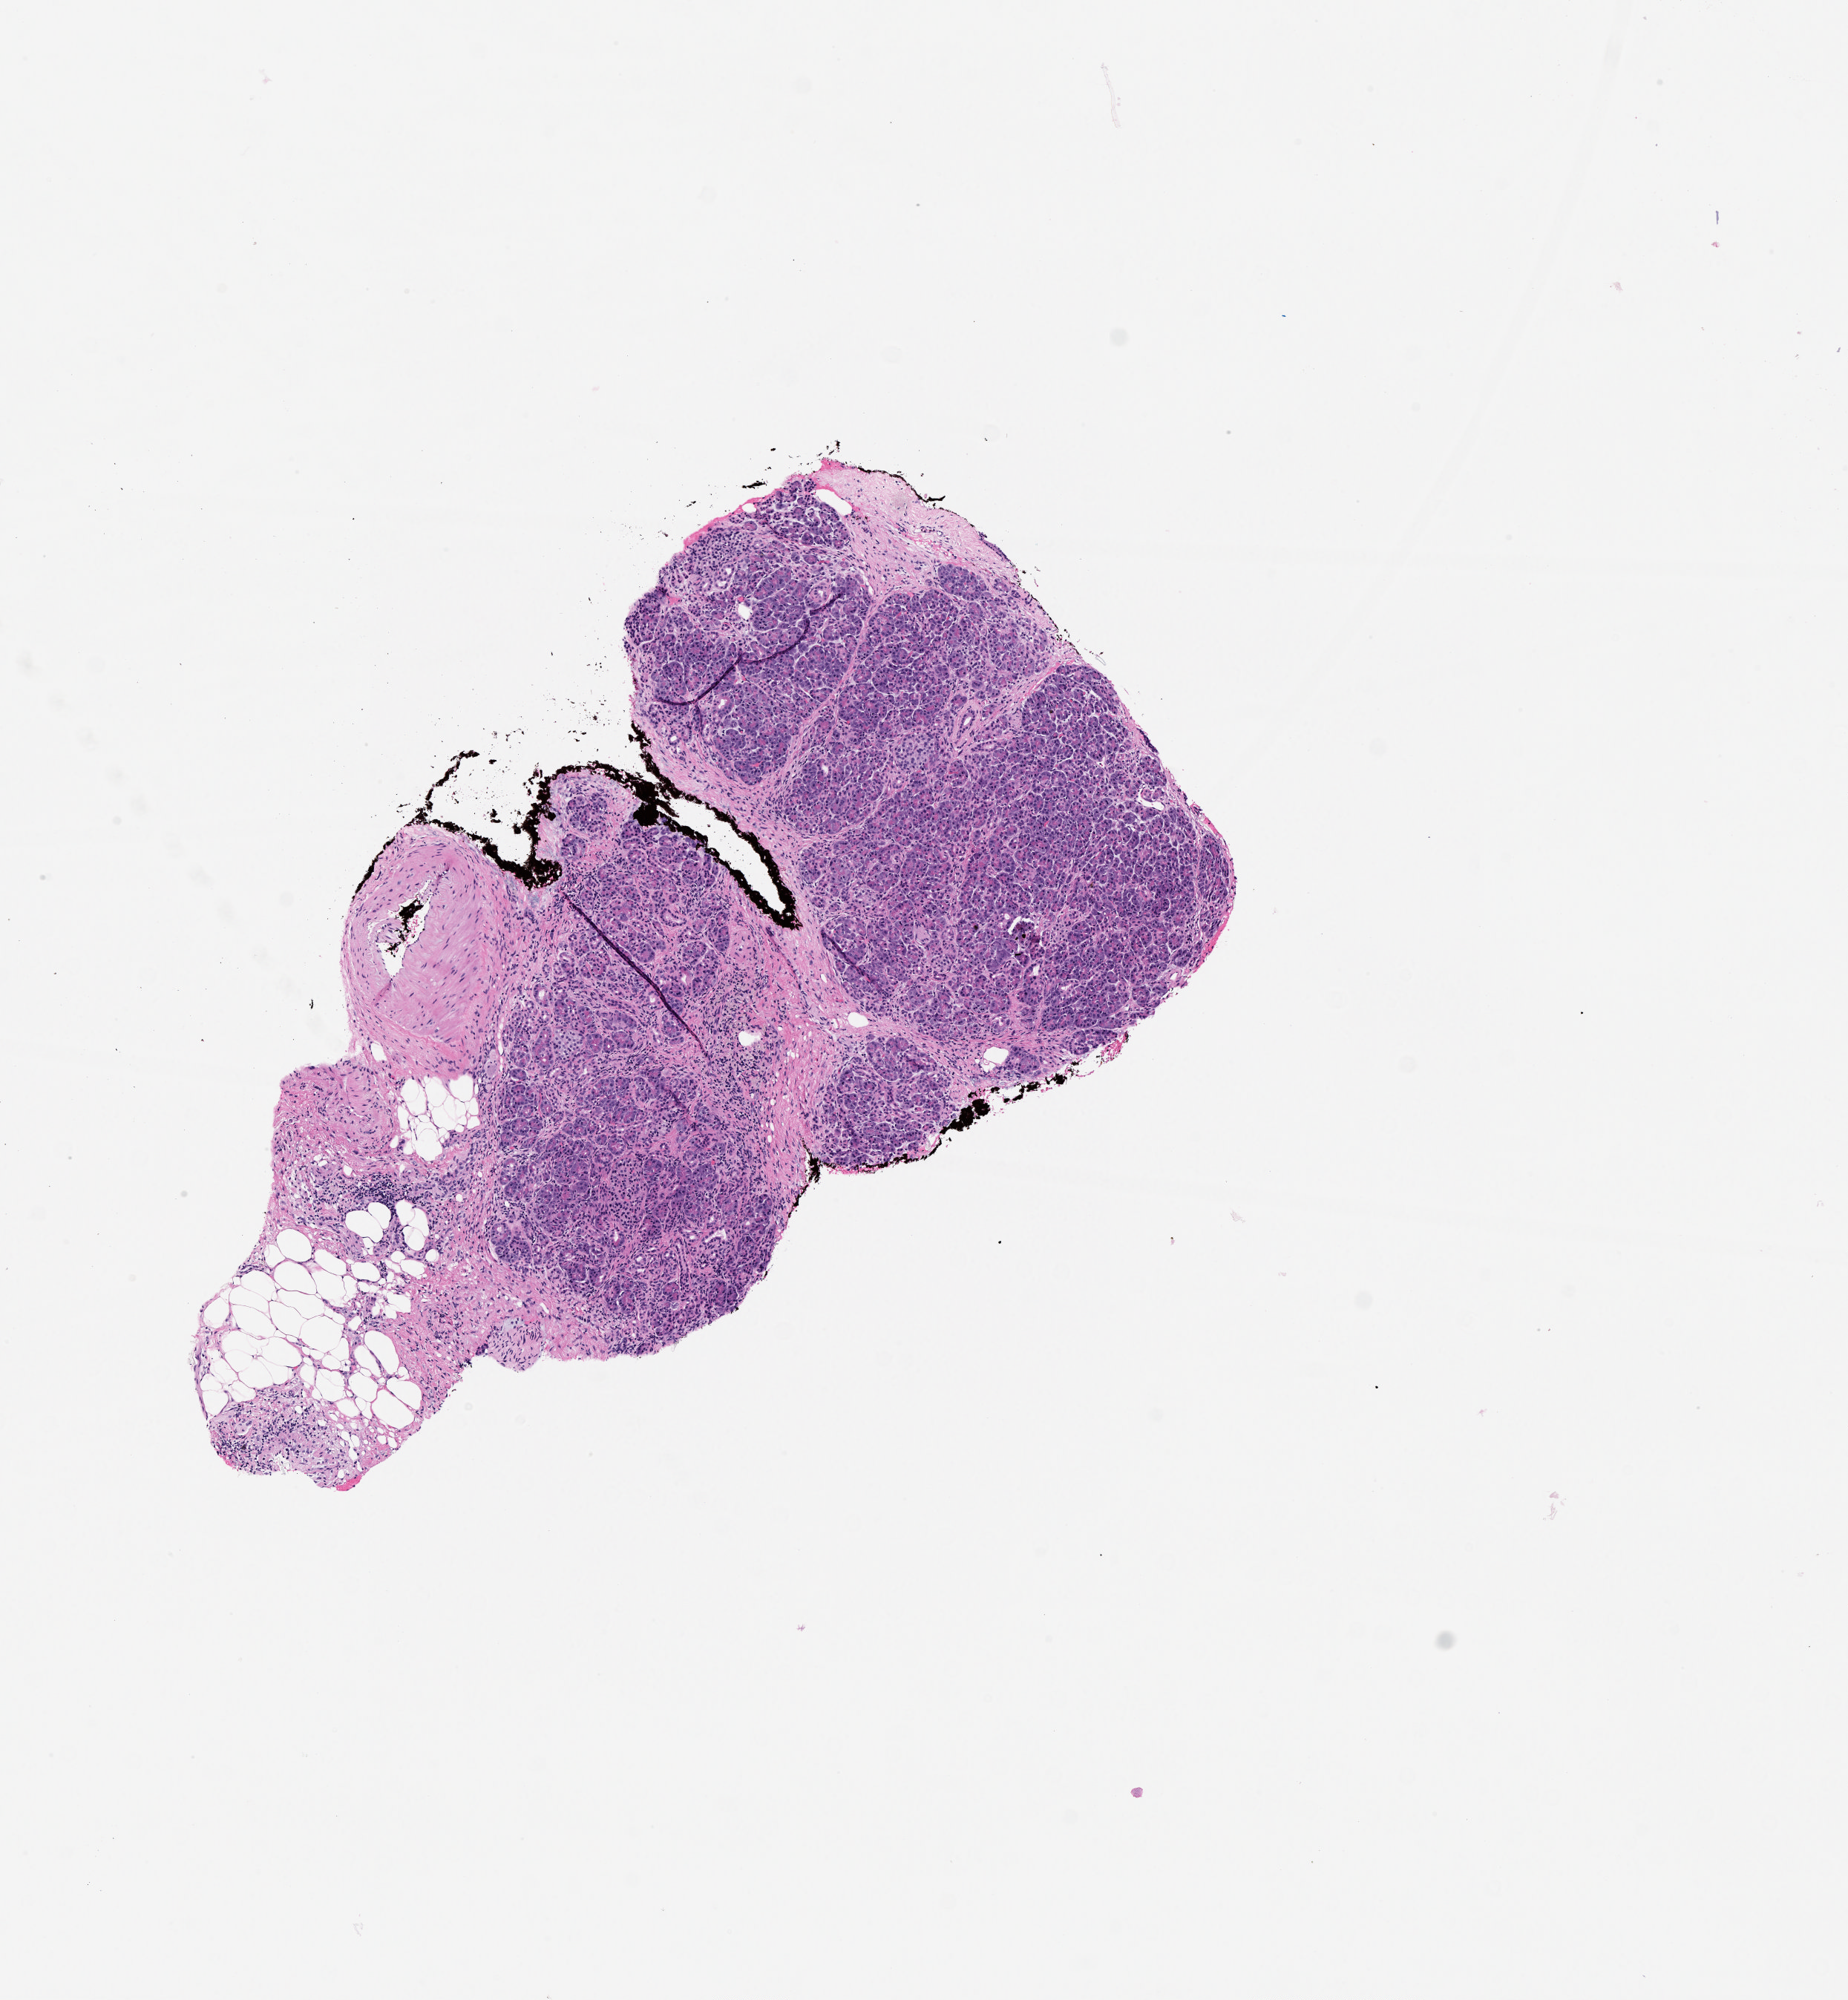
Whole-slide histology image, Hematoxylin and eosin (H&E) stained, low-resolution overview of the scanned area, about 5.0 x 5.4 mm; normal (non-tumour) tissue sample, pancreas. 85-year-old female patient.
• this section: normal (non-tumour) tissue from the same patient
• patient diagnosis: Infiltrating duct carcinoma, NOS